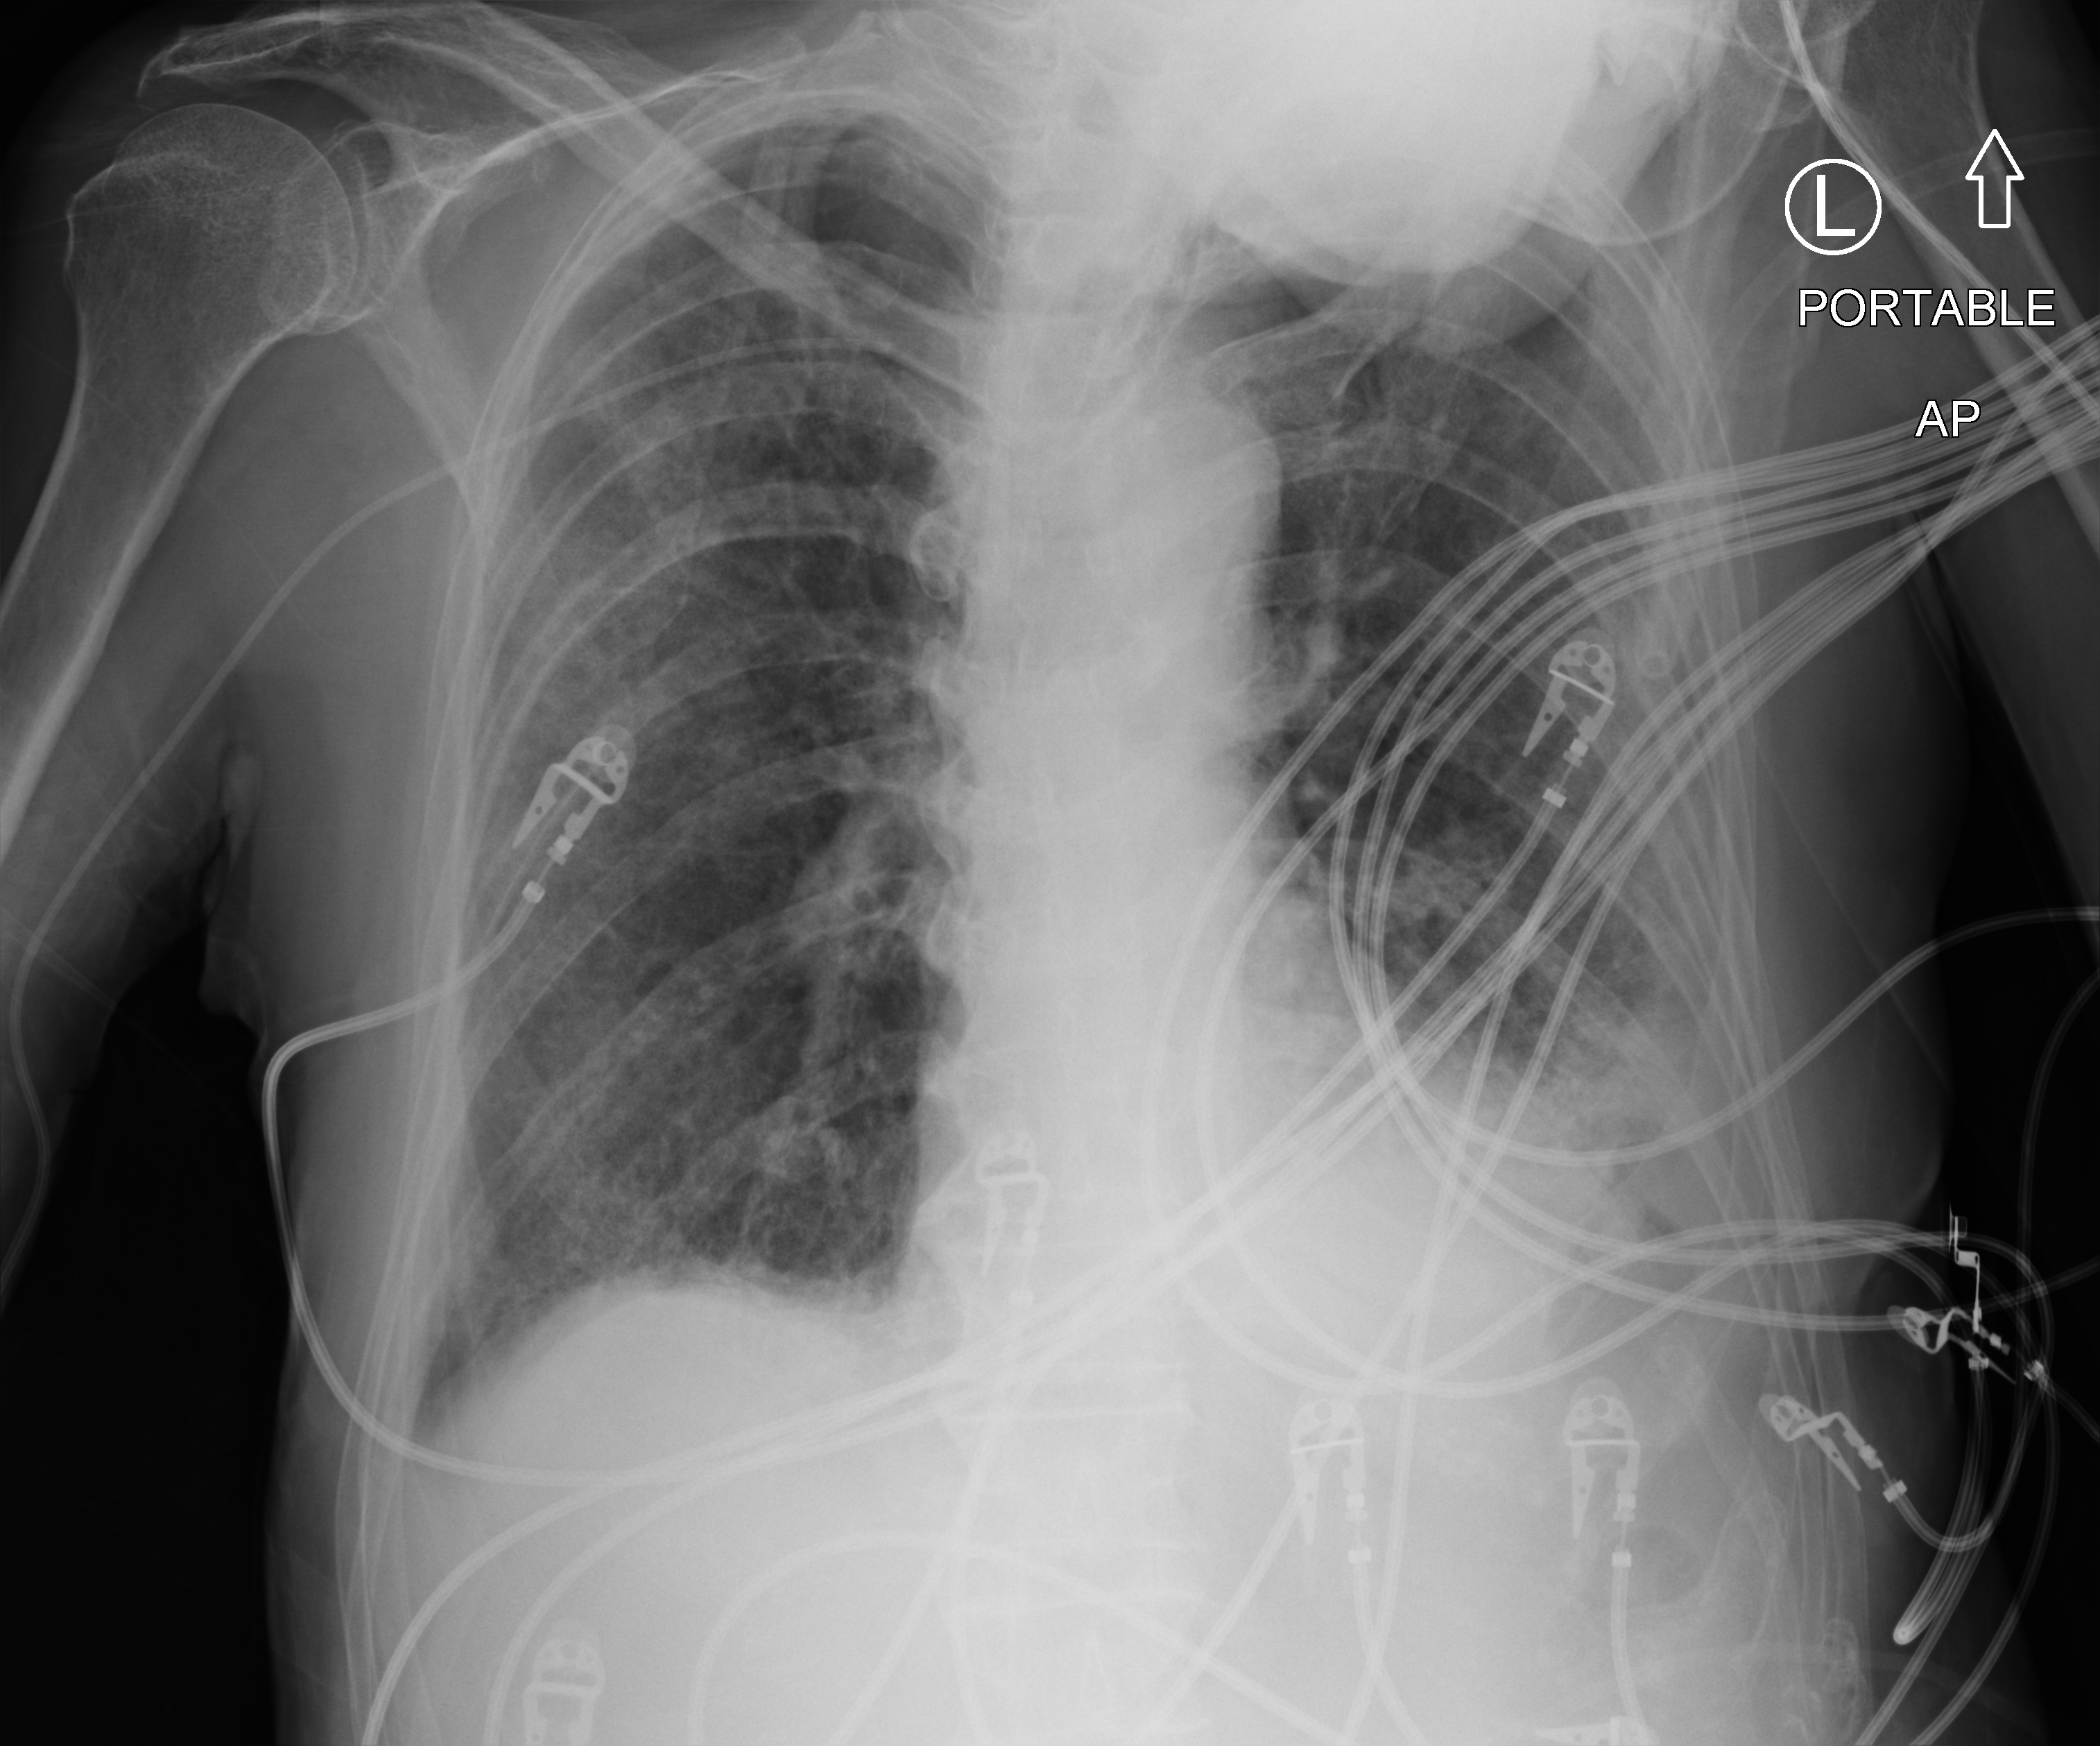
Portable chest radiograph; anteroposterior (AP) projection. Male patient hospitalised with COVID-19, age 60–74 years.
From the hospital-stay record, not from the radiograph (when in the stay this image was taken is not recorded): mechanically ventilated during this hospital stay: yes.